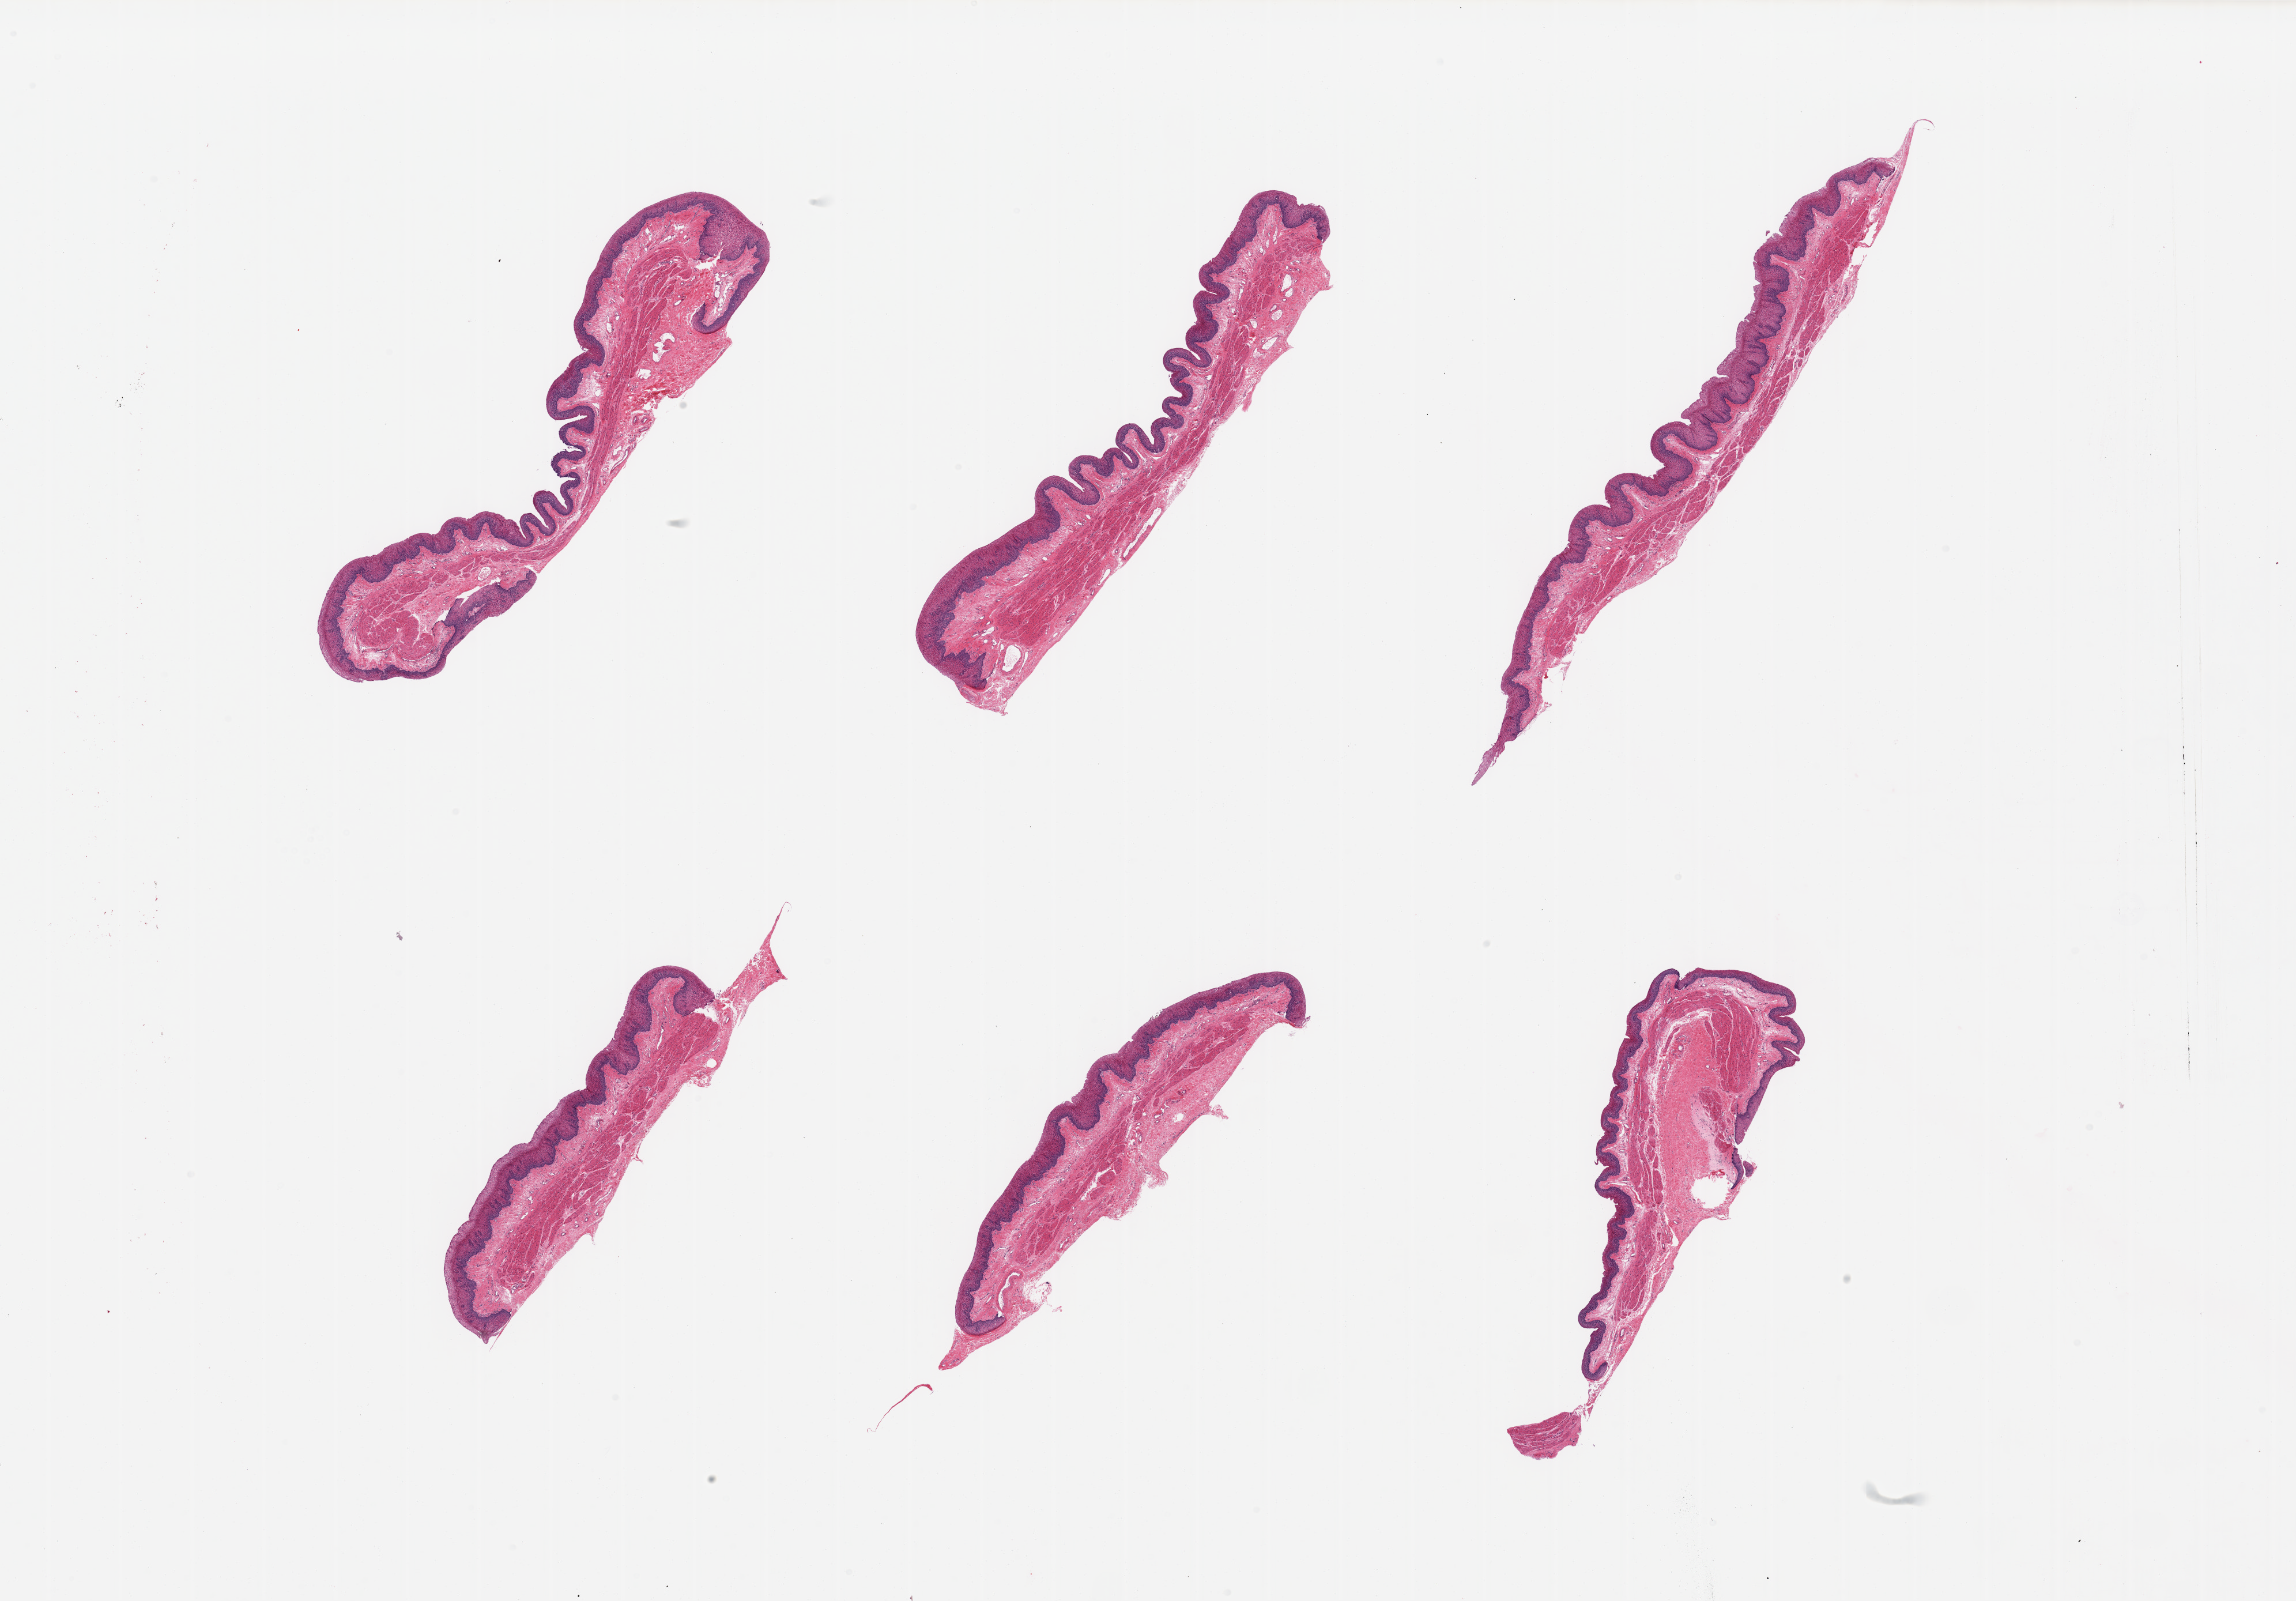
Haematoxylin and eosin whole-slide image, brightfield — low-resolution overview of the scanned area, about 31.5 x 22.0 mm (acquisition: 20x scan); PAXgene-fixed paraffin-embedded (PFPE) section; section of esophageal mucous membrane (target tissue); donor tissue sample. Donor: female.
Reviewer comment on this tissue sample: 6 pieces.